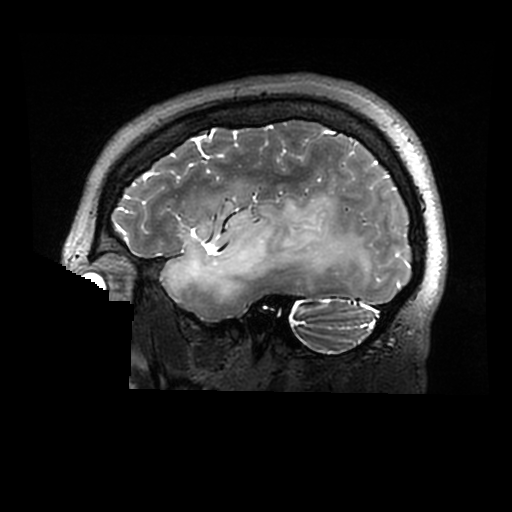
Brain MRI from a brain-tumour surgery series, one sagittal slice. Position 224 of 320 along the scan axis. 0.6 mm slice thickness. 512 × 512 image matrix, field of view 240 × 240 mm. From the clinical record (not read from this slice): histopathology: Astrocytoma; WHO grade: 2; IDH mutation: yes.
Outlined on this slice (expert manual segmentation):
- tumour: bounding box [x1, y1, x2, y2] px = [163, 194, 381, 303]